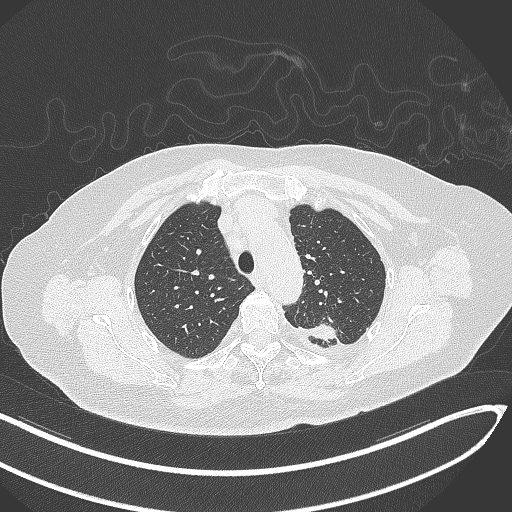
Chest CT, one axial slice; slice 246 of 270 in the series (ordered by position); reconstruction kernel B70f; lung window (W 1500 / L -600 HU); 1 mm slice thickness; 512 × 512 image matrix, field of view 400 × 400 mm. Patient: female, 76 years. From the clinical record (not read from this slice): clinical TNM (as recorded): T1c N0 M0.
Outlined on this slice (bounding box drawn by a radiologist):
- lung tumour (recorded histology: adenocarcinoma): box from (x=298, y=317) to (x=342, y=346) px